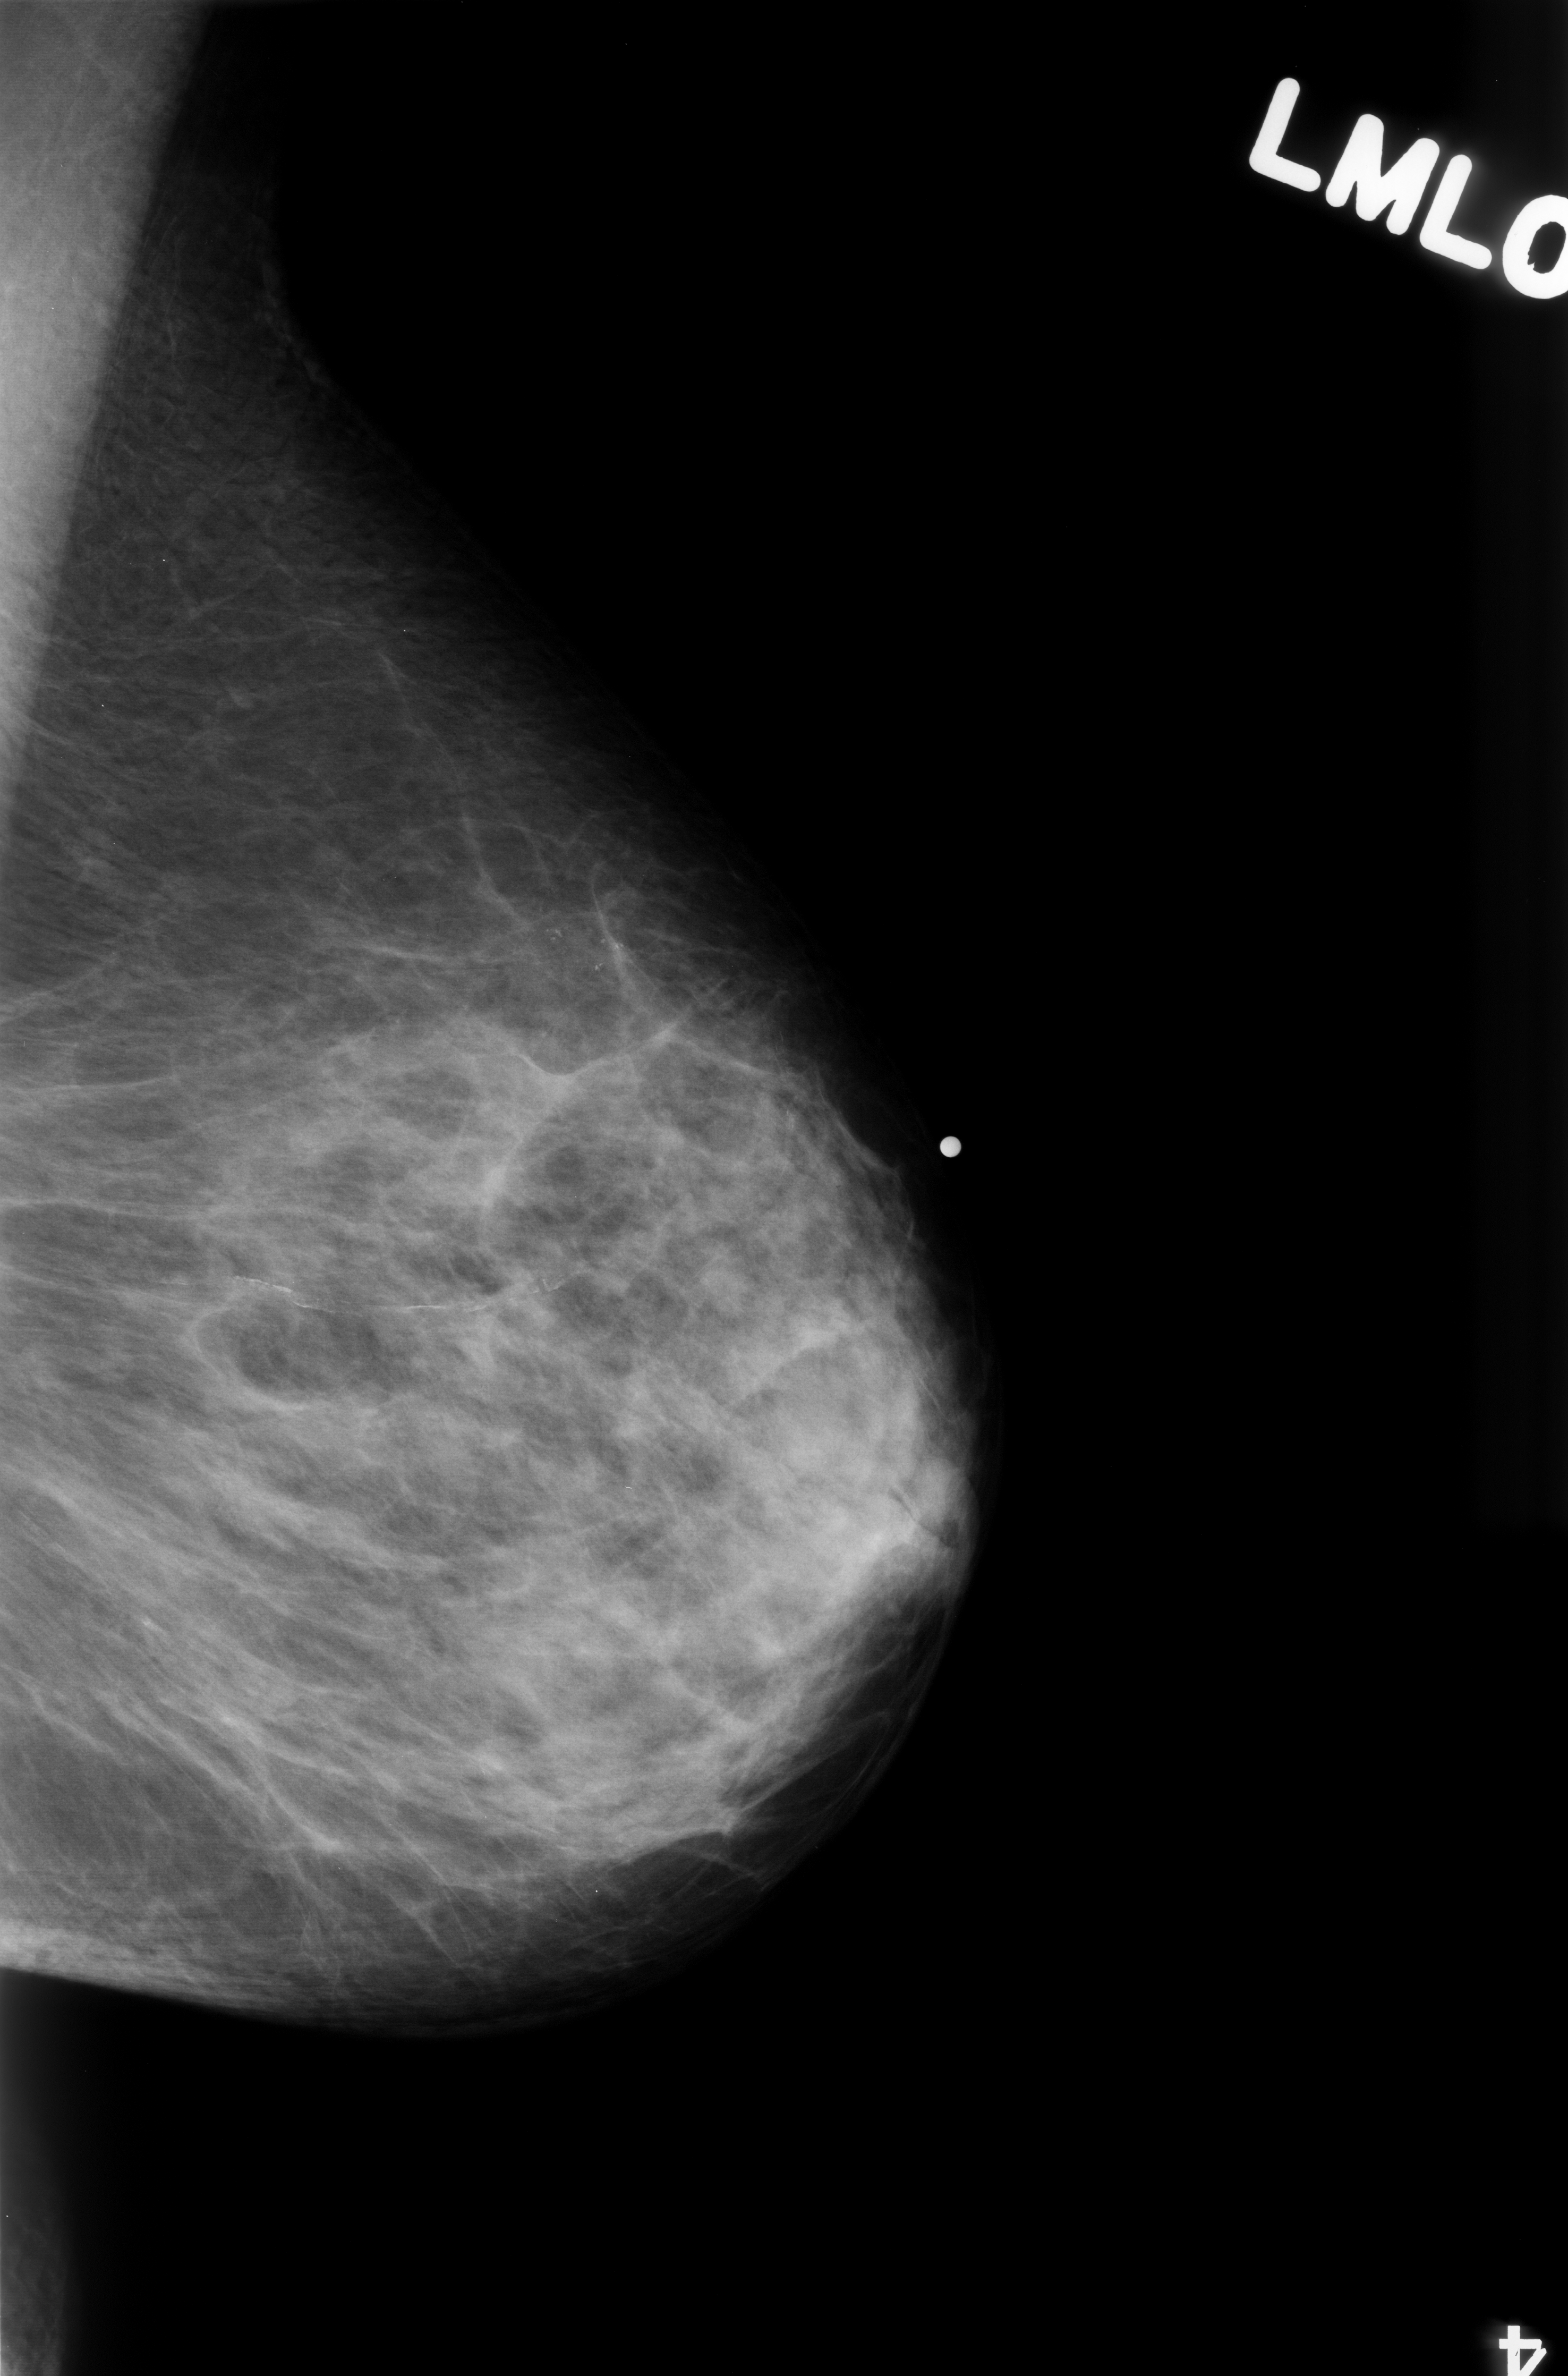
Mammogram (digitized film). Left breast. Mediolateral oblique (MLO) view. Breast composition: scattered fibroglandular densities (BI-RADS density category 2 of 4). 1568 × 2376 image matrix.
Expert-marked regions of interest on this image (one box per marked abnormality):
- calcifications, morphology pleomorphic, distribution clustered; BI-RADS assessment category 4; subtlety rating 3 on a 1 (subtle) to 5 (obvious) scale; pathology result (as recorded, not read from the image): benign: bounding box [x1, y1, x2, y2] px = [458, 833, 689, 1051]